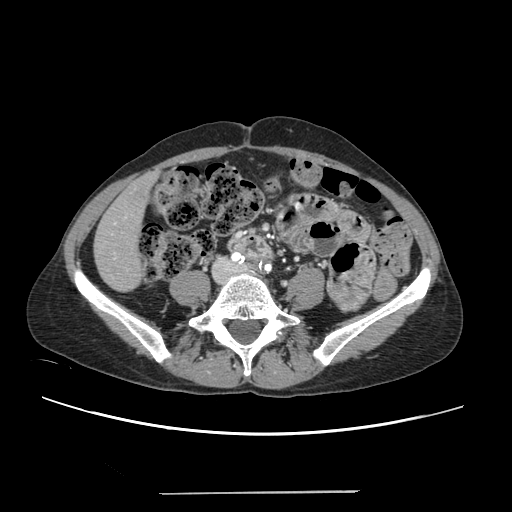
Contrast-enhanced abdominal CT, one axial slice. Position 34 of 240 along the scan axis. 120 kVp. Intravenous contrast given. Soft-tissue window (W 400 / L 40 HU). 1.25 mm slice thickness. 512 × 512 image matrix, field of view 371 × 371 mm. Female patient, age 60 years. Case-level facts recorded for this patient, not image findings: diagnosis: colorectal cancer liver metastases, imaged before liver resection.
Outlined on this slice (outlined manually by an expert reader):
- liver: bounding box <95,175,154,291> (left, top, right, bottom; pixels)
- planned liver remnant (the part of the liver to remain after resection): <95,176,153,291>
- portal vein (with intrahepatic branches): <112,217,126,258>